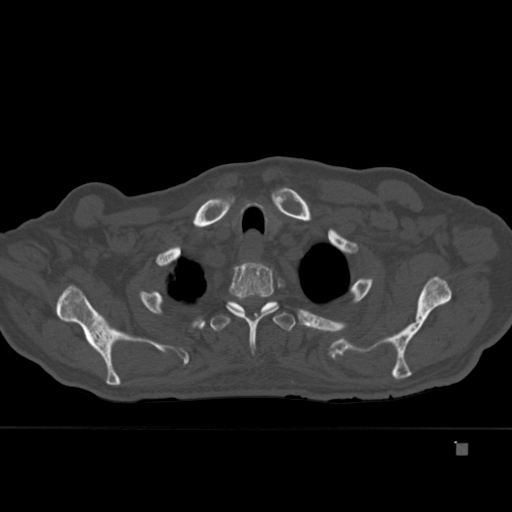
CT including the spine, one axial slice. Slice 343 of 451 in the series (ordered by position). Bone window (W 1800 / L 400 HU). 1.5 mm slice thickness. 512 × 512 image matrix, field of view 378 × 378 mm. Male patient, age 75 years. From the clinical record (not read from this slice): primary cancer: prostate.
Structures marked on this image (semi-automatic segmentation, software-assisted and operator-edited):
- T2 vertebra: bounding box (x1, y1, x2, y2) in pixels: (226, 262, 279, 355)
- T3 vertebra: (210, 301, 296, 331)